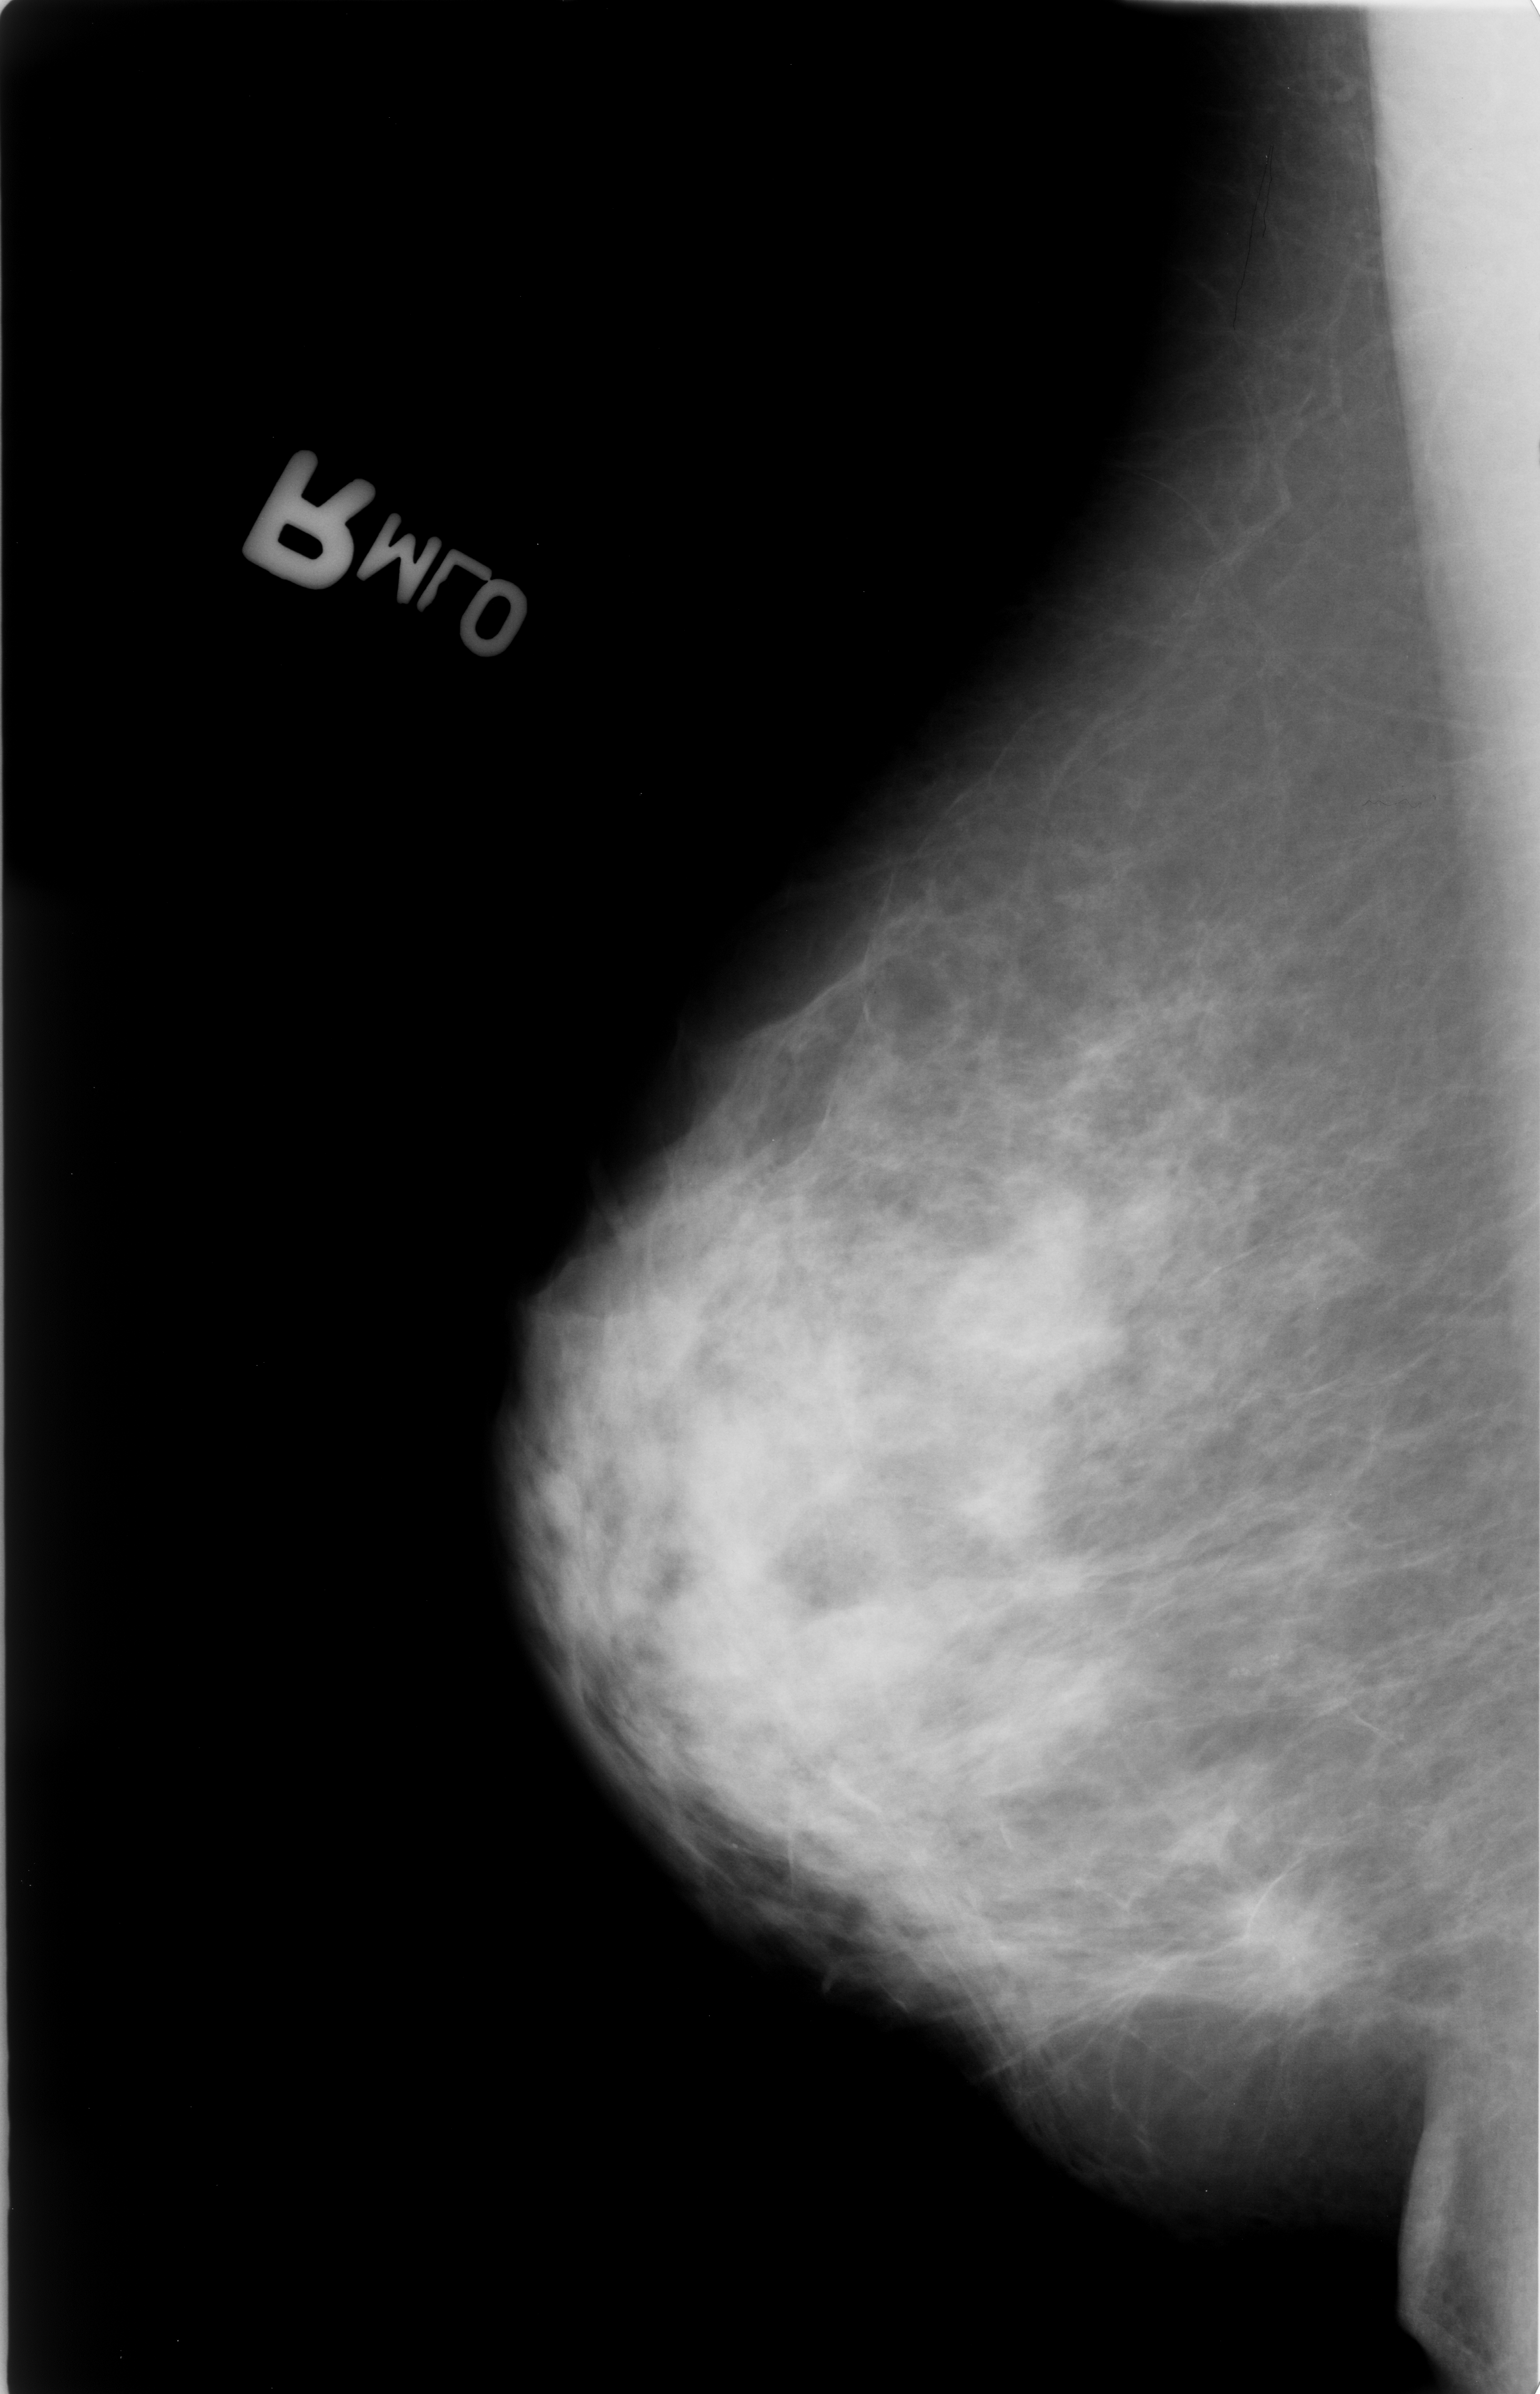
Mammogram (digitized film); right breast; MLO view.
- Finding: calcifications, morphology punctate, distribution clustered; BI-RADS assessment category 5; pathology (as recorded): malignant.